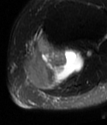
MRI of an extremity soft-tissue mass, one axial slice; position 46 of 78 along the scan axis; T2-weighted fat-saturated; MR volume resampled by the dataset authors to the PET/CT grid (not the native acquisition matrix); 107 × 125 image matrix, field of view 104 × 122 mm. Female patient. Case-level facts recorded for this patient, not image findings: histological type: extraskeletal high grade osteogenic sarcoma; grade: high; site of the primary tumour: left calf.
Structures marked on this image (expert contour drawn on MRI and transferred to this co-registered scan by the dataset authors):
- gross tumour volume (mass): box from (x=25, y=43) to (x=86, y=90) px